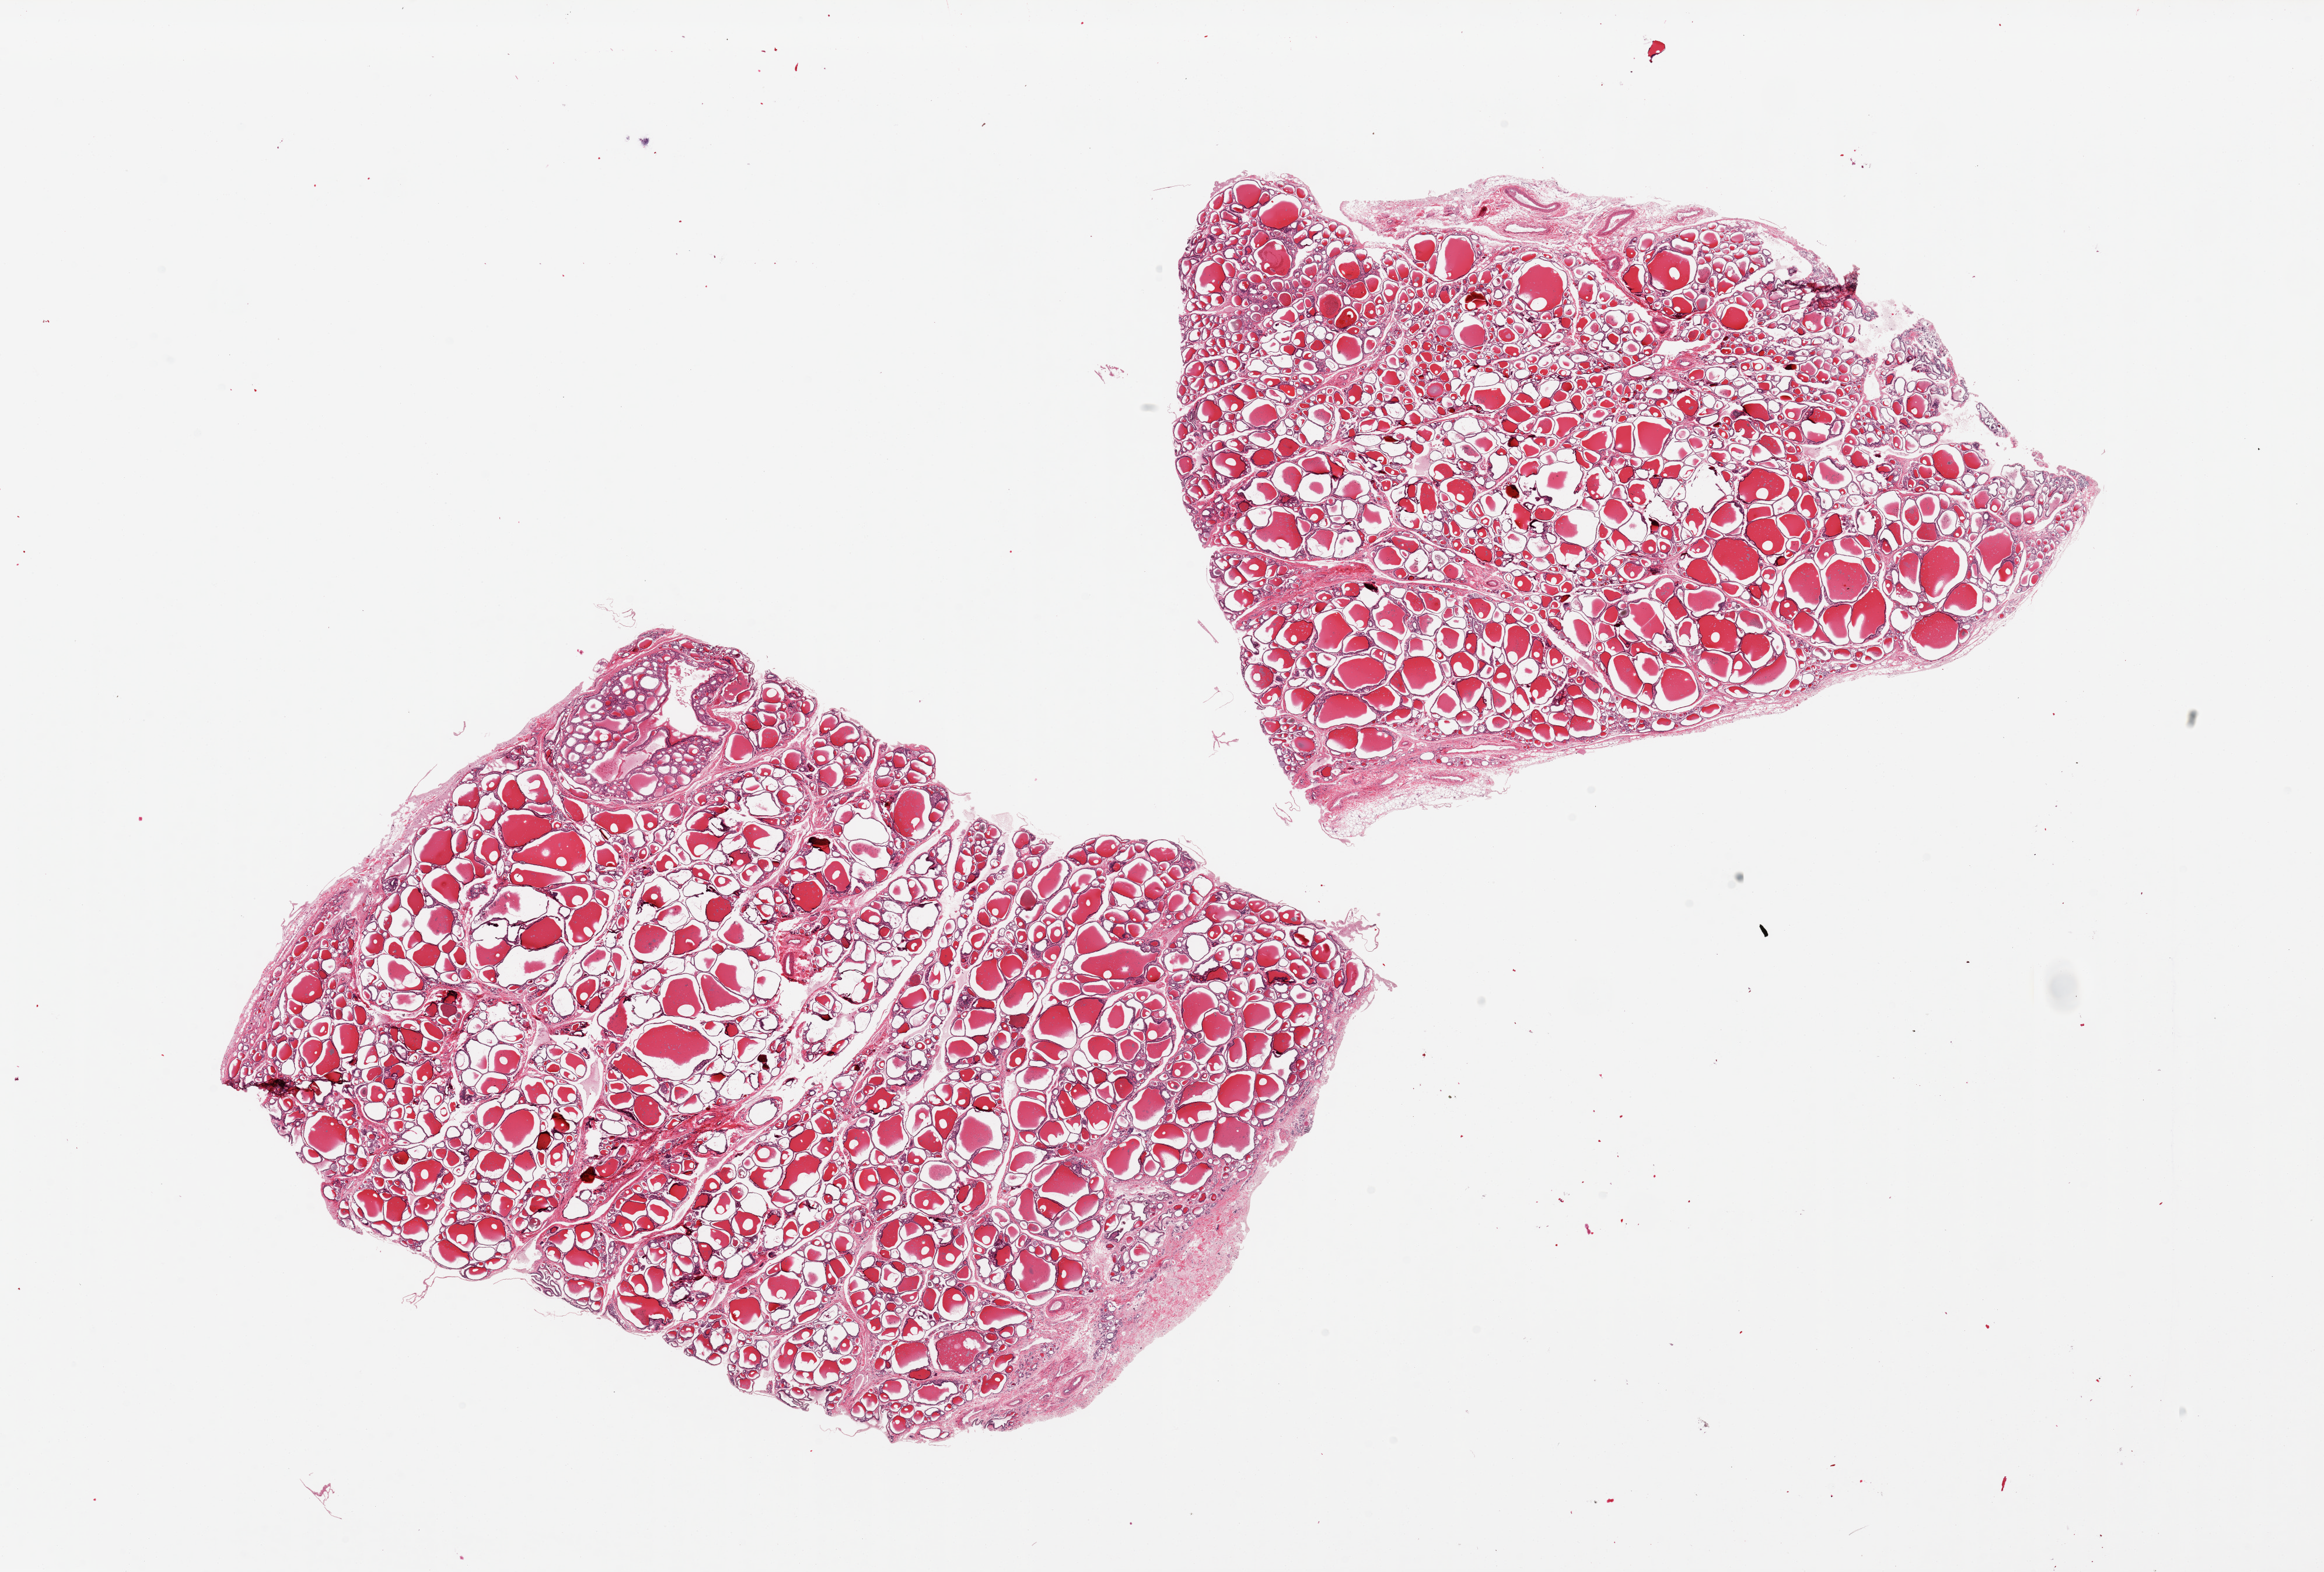
Hematoxylin and eosin (H&E) whole-slide image, low-resolution overview of the scanned area, about 31.5 x 21.3 mm (acquisition: 20x scan); PAXgene-fixed, paraffin-embedded tissue; target tissue: thyroid; donor tissue sample.
* reviewer comment on this tissue sample: 2 pieces, mulitnodular goiter